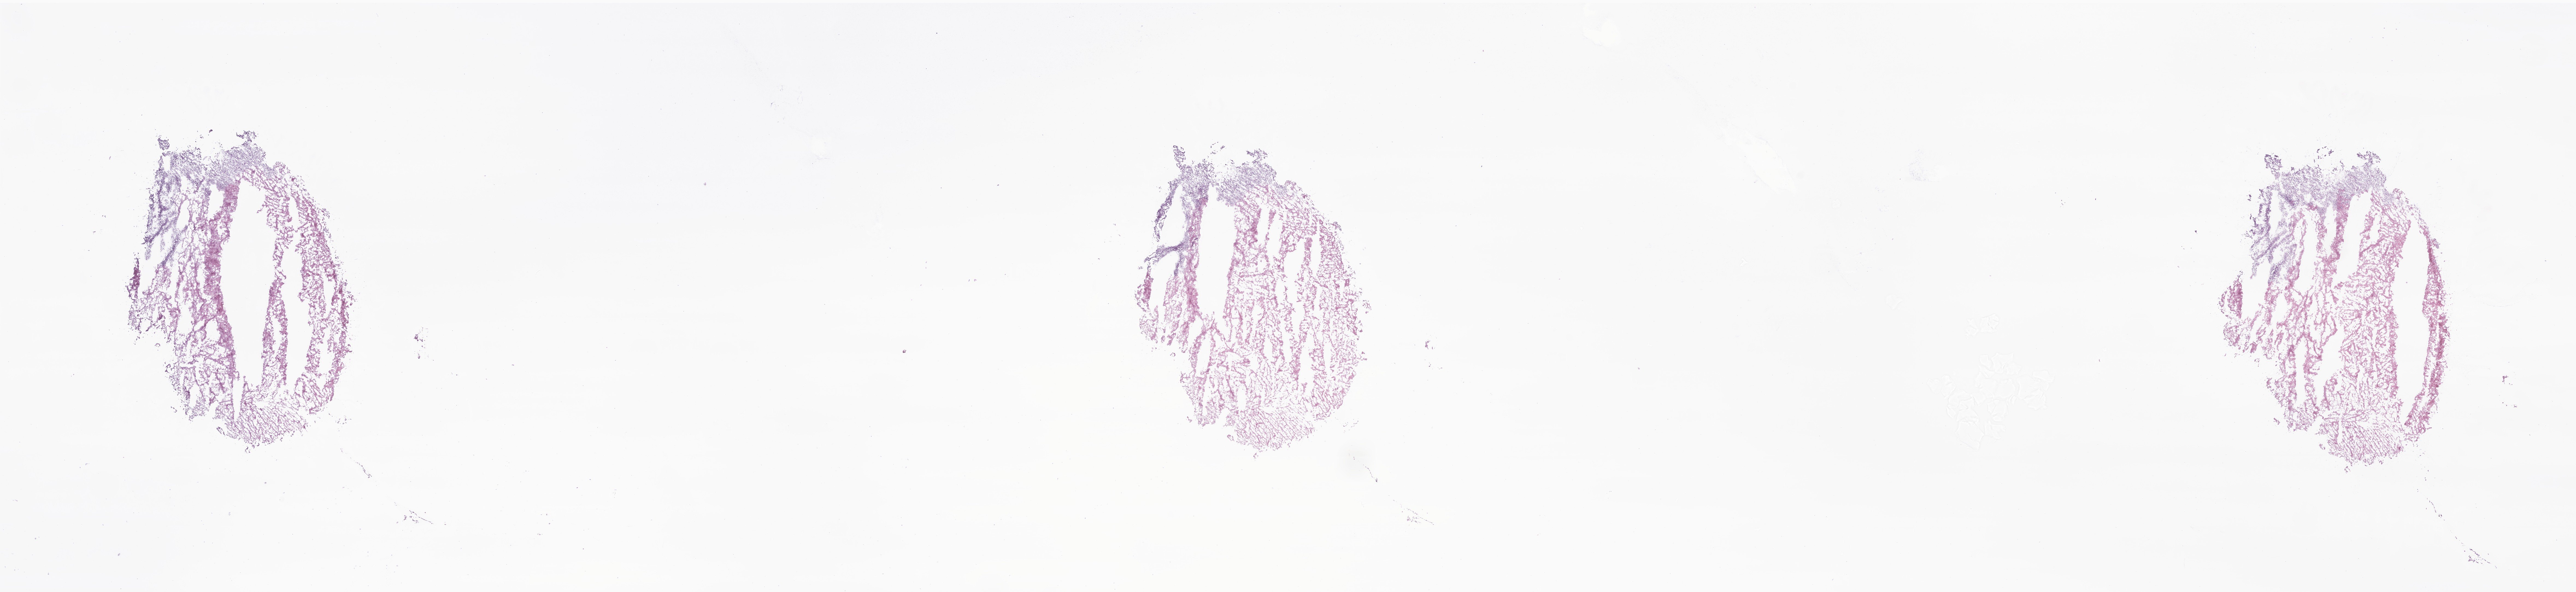
H&E whole-slide image of tumor tissue from the brain — low-resolution overview of the scanned area, about 39.7 x 9.1 mm, cryosection (OCT / tissue freezing medium). Female patient, age 88 months (7 years 4 months).
Diagnosis: Neoplasm, malignant.